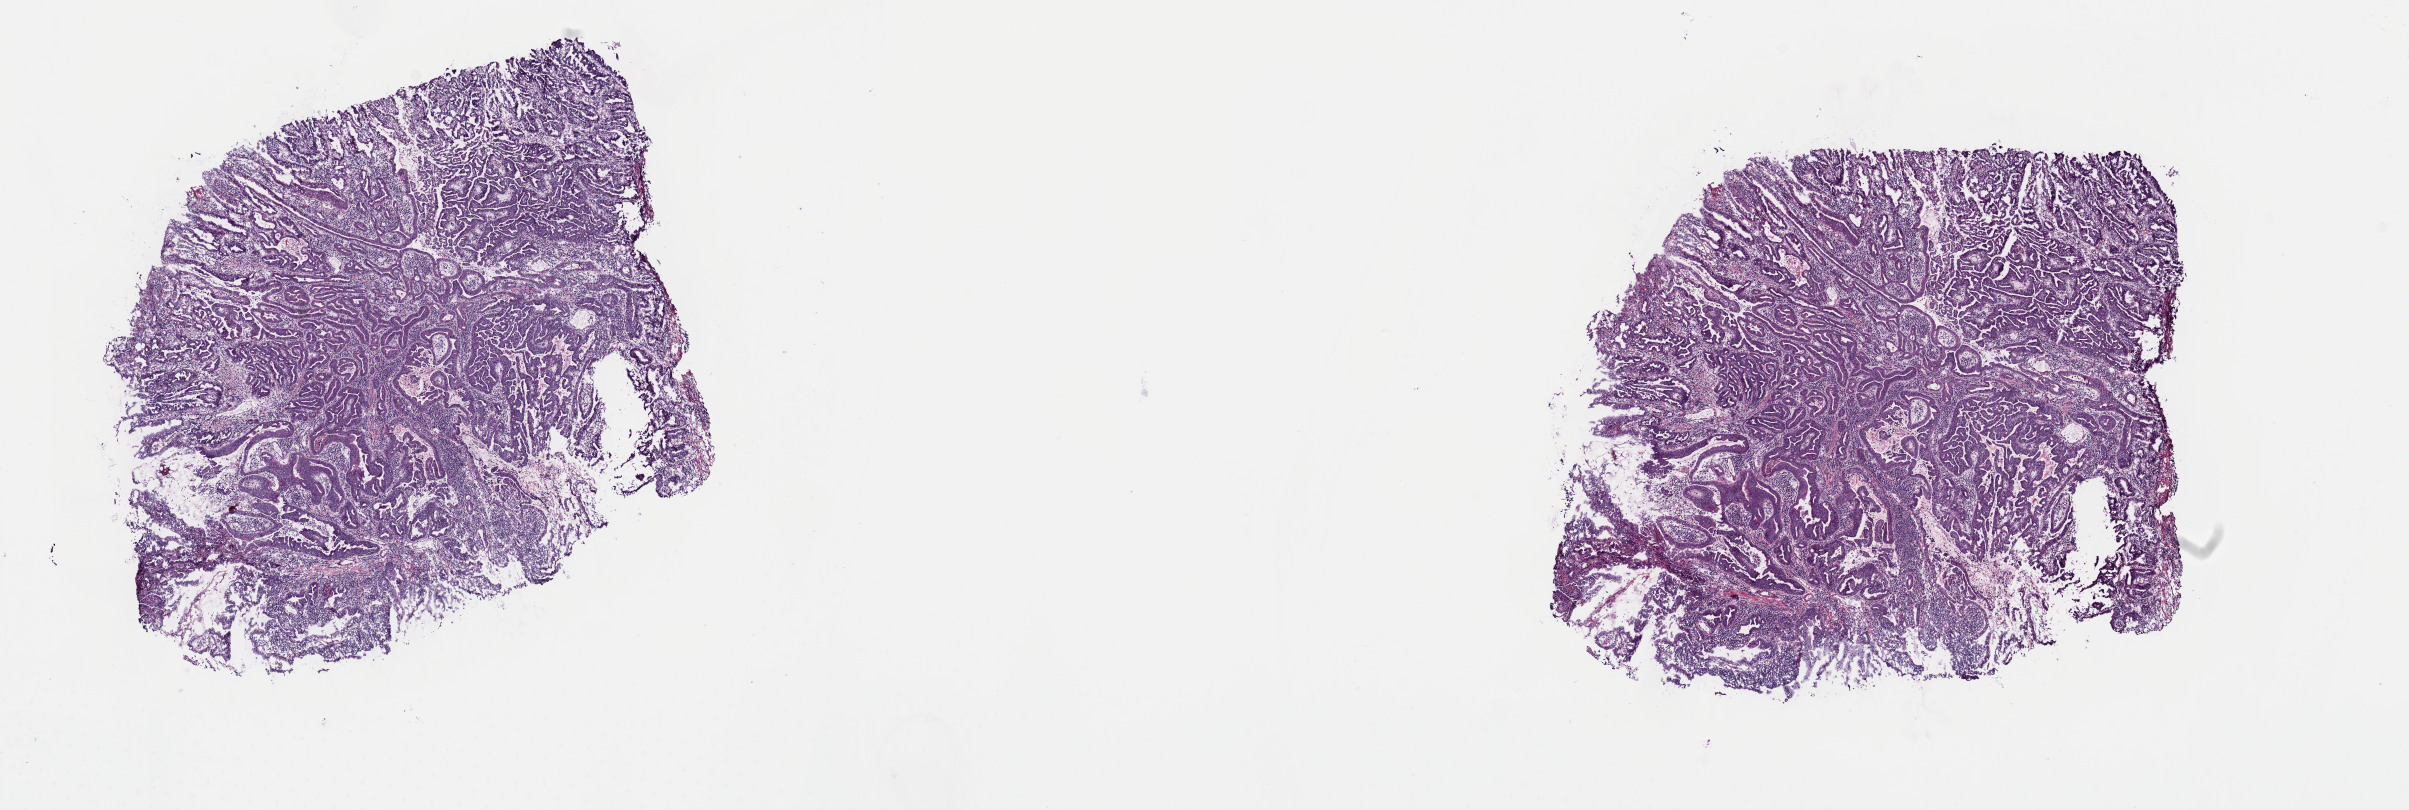
H&E-stained whole-slide image, shown as a low-resolution overview of the whole scanned area (about 19.0 x 6.4 mm, slide scanned at 40x); frozen section from the top of the tissue portion; sample: primary tumour, esophagus. Female patient; age at initial diagnosis 70 years. Histologic grade: G3 (poorly differentiated). Slide review estimates, as recorded: tumour cells 95%, tumour nuclei 70%, normal cells 0%, stromal cells 5%, necrosis 0%. Infiltration values recorded for this section: lymphocyte infiltration 0%, monocyte infiltration 0%, neutrophil infiltration 0%.
AJCC pathologic stage: I (7th edition). Pathologic diagnosis: Adenocarcinoma, NOS (lower third of esophagus). Lymph nodes positive (case pathology): 0 of 16 examined.